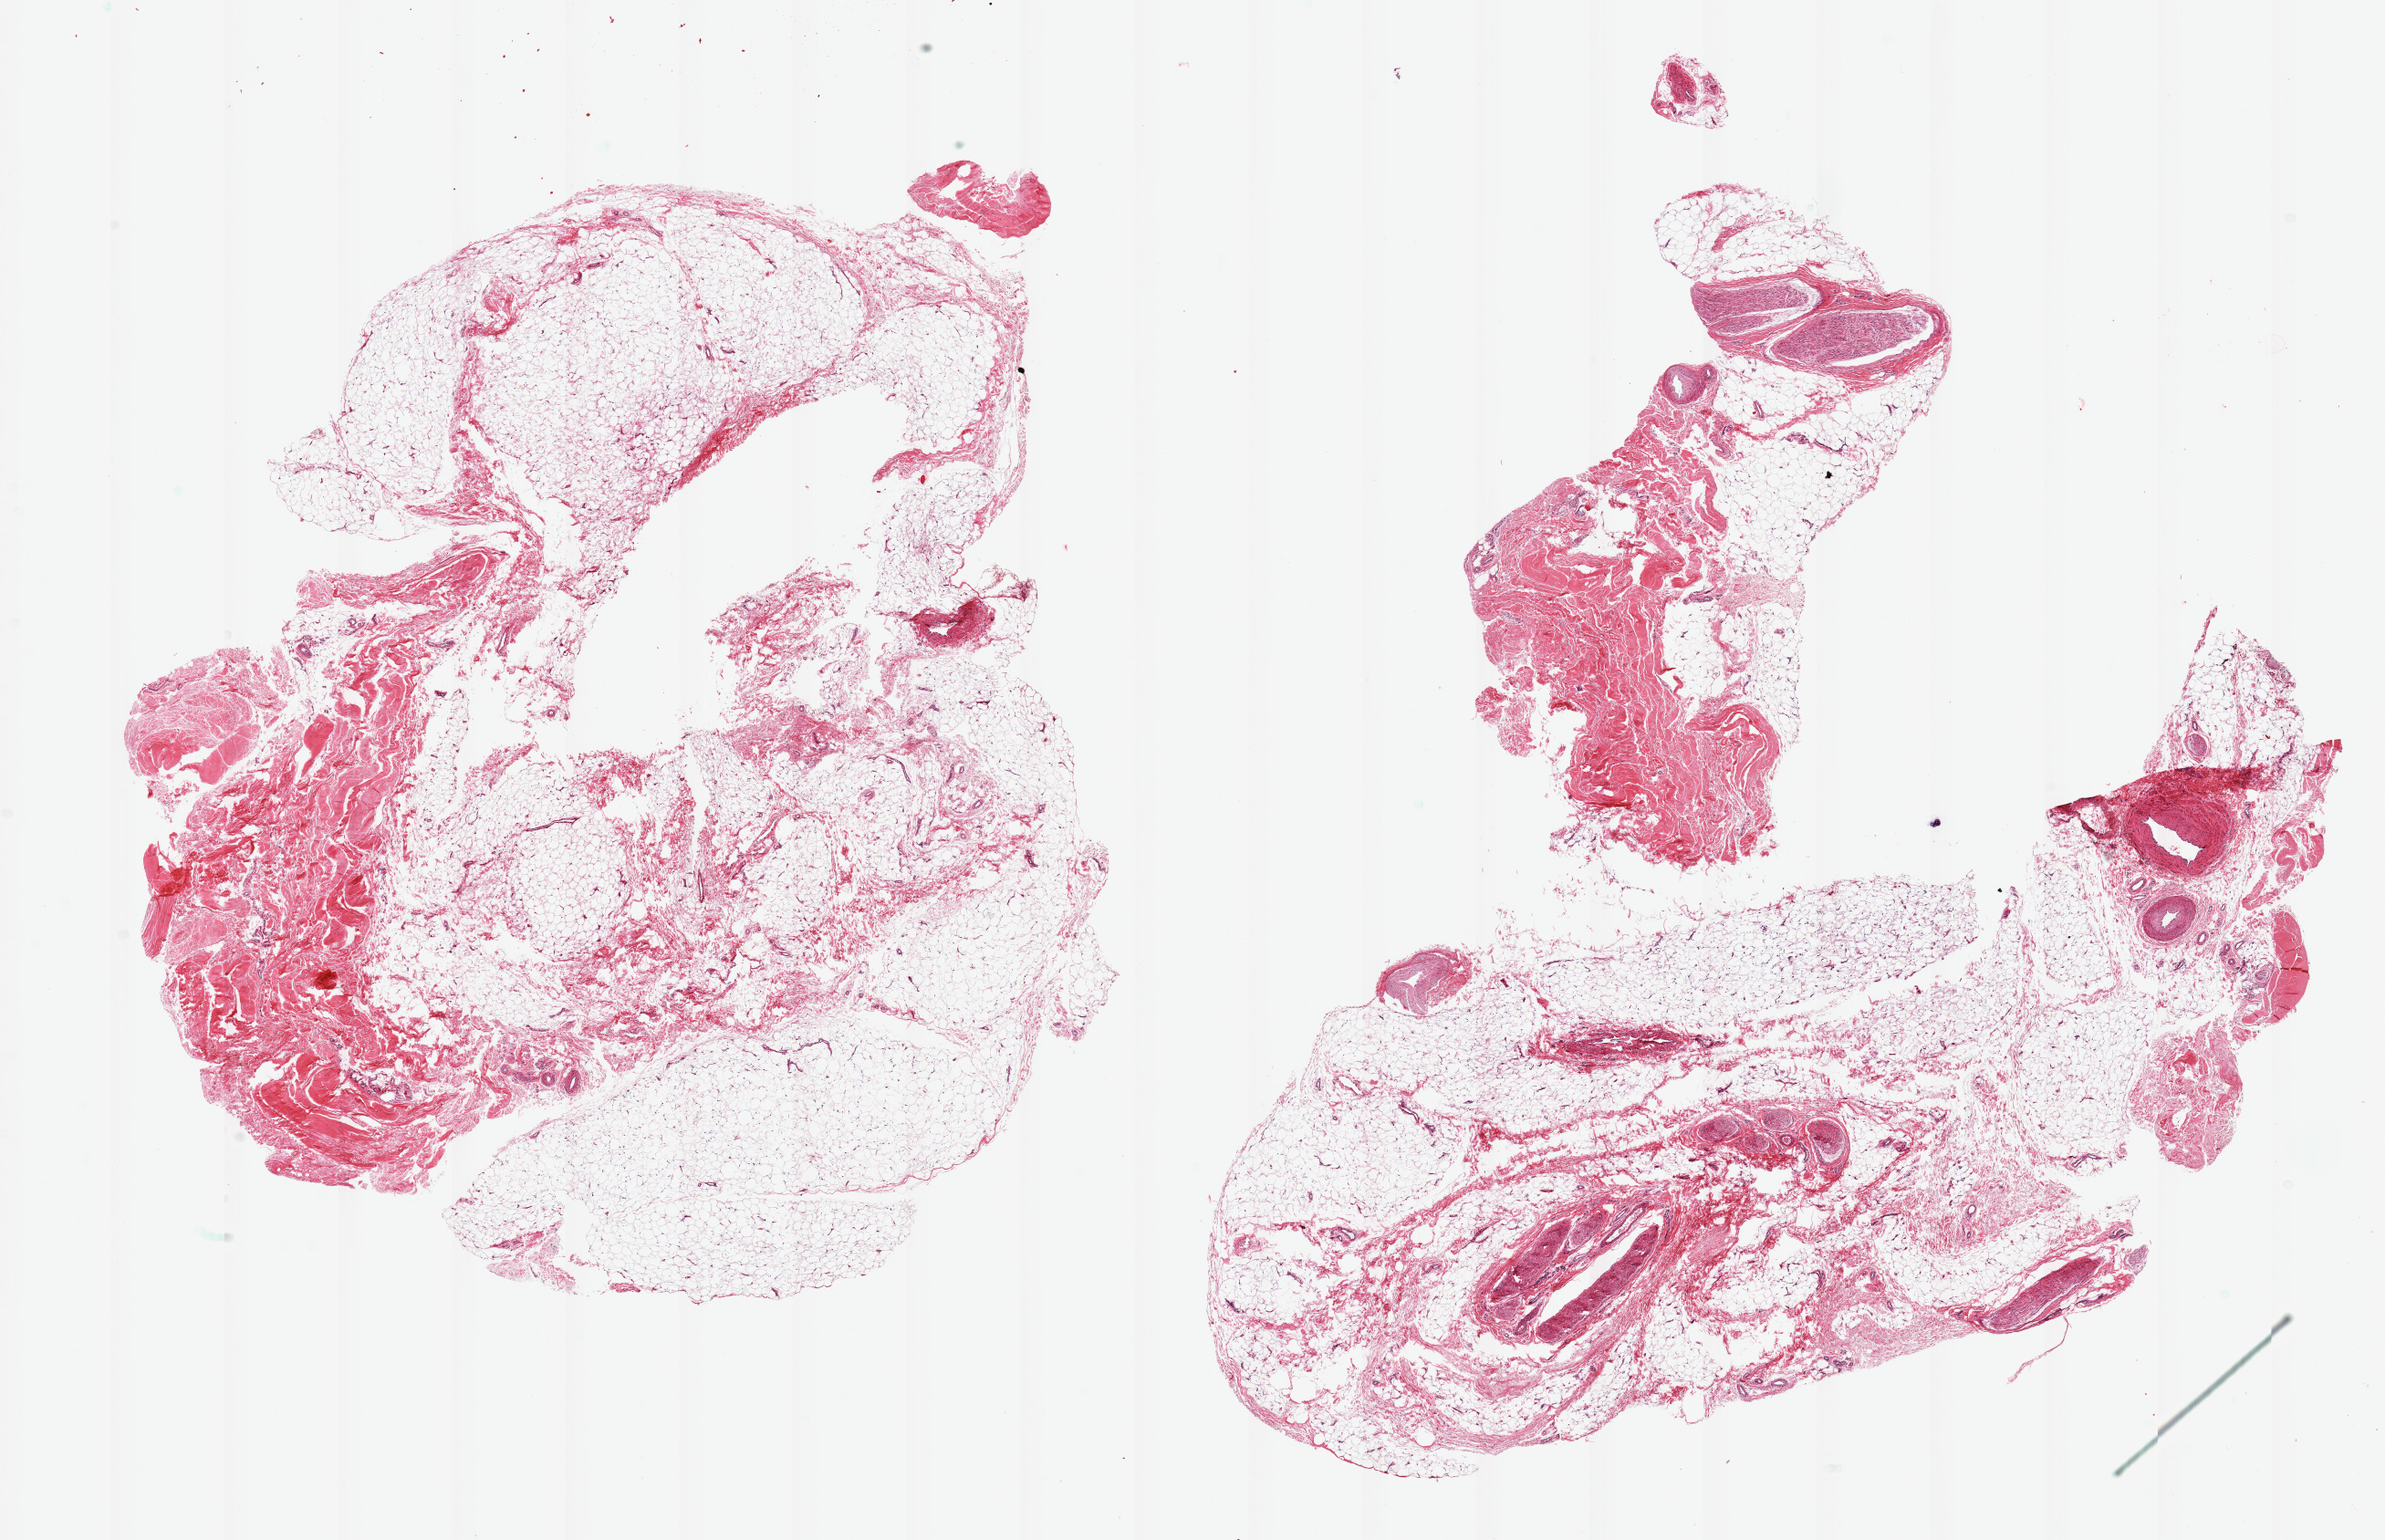
Digitized haematoxylin and eosin-stained section — low-resolution overview of the scanned area, about 20.7 x 13.3 mm, PAXgene-fixed paraffin-embedded (PFPE) section, sampled site (target tissue): adipose tissue, tissue donor sample.
- review note (as recorded): 2 pieces; adipose tissue with 30-50% vessels/nerve/connective tissue